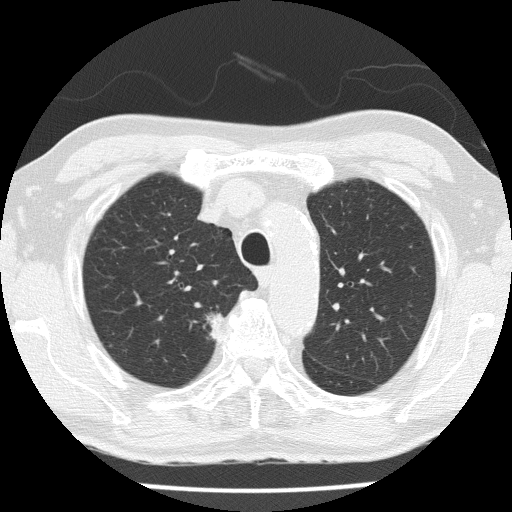
Low-dose screening chest CT, one axial slice; slice 113 of 153 in the series (ordered by position); reconstruction kernel FC51; lung window (W 1500 / L -600 HU); 512 × 512 image matrix, field of view 323 × 323 mm.
Outlined on this slice (manually delineated by an expert):
- lesion 1 (tumor, upper lobe of right lung): bounding box <194,314,222,339> (left, top, right, bottom; pixels)